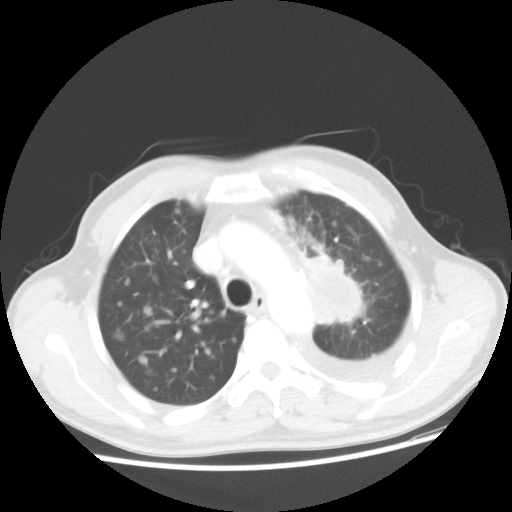
Chest CT, one axial slice. Slice 35 of 48 in the series (ordered by position). 100 kVp. Lung window (W 1500 / L -600 HU). 512 × 512 image matrix. Male patient, age 55 years. Case-level facts recorded for this patient, not image findings: clinical TNM (as recorded): T2 N3 M1a; histopathological grade: G3.
Structures marked on this image (bounding box drawn by a radiologist):
- lung tumour (recorded histology: squamous cell carcinoma): bounding box [x1, y1, x2, y2] px = [304, 246, 370, 333]